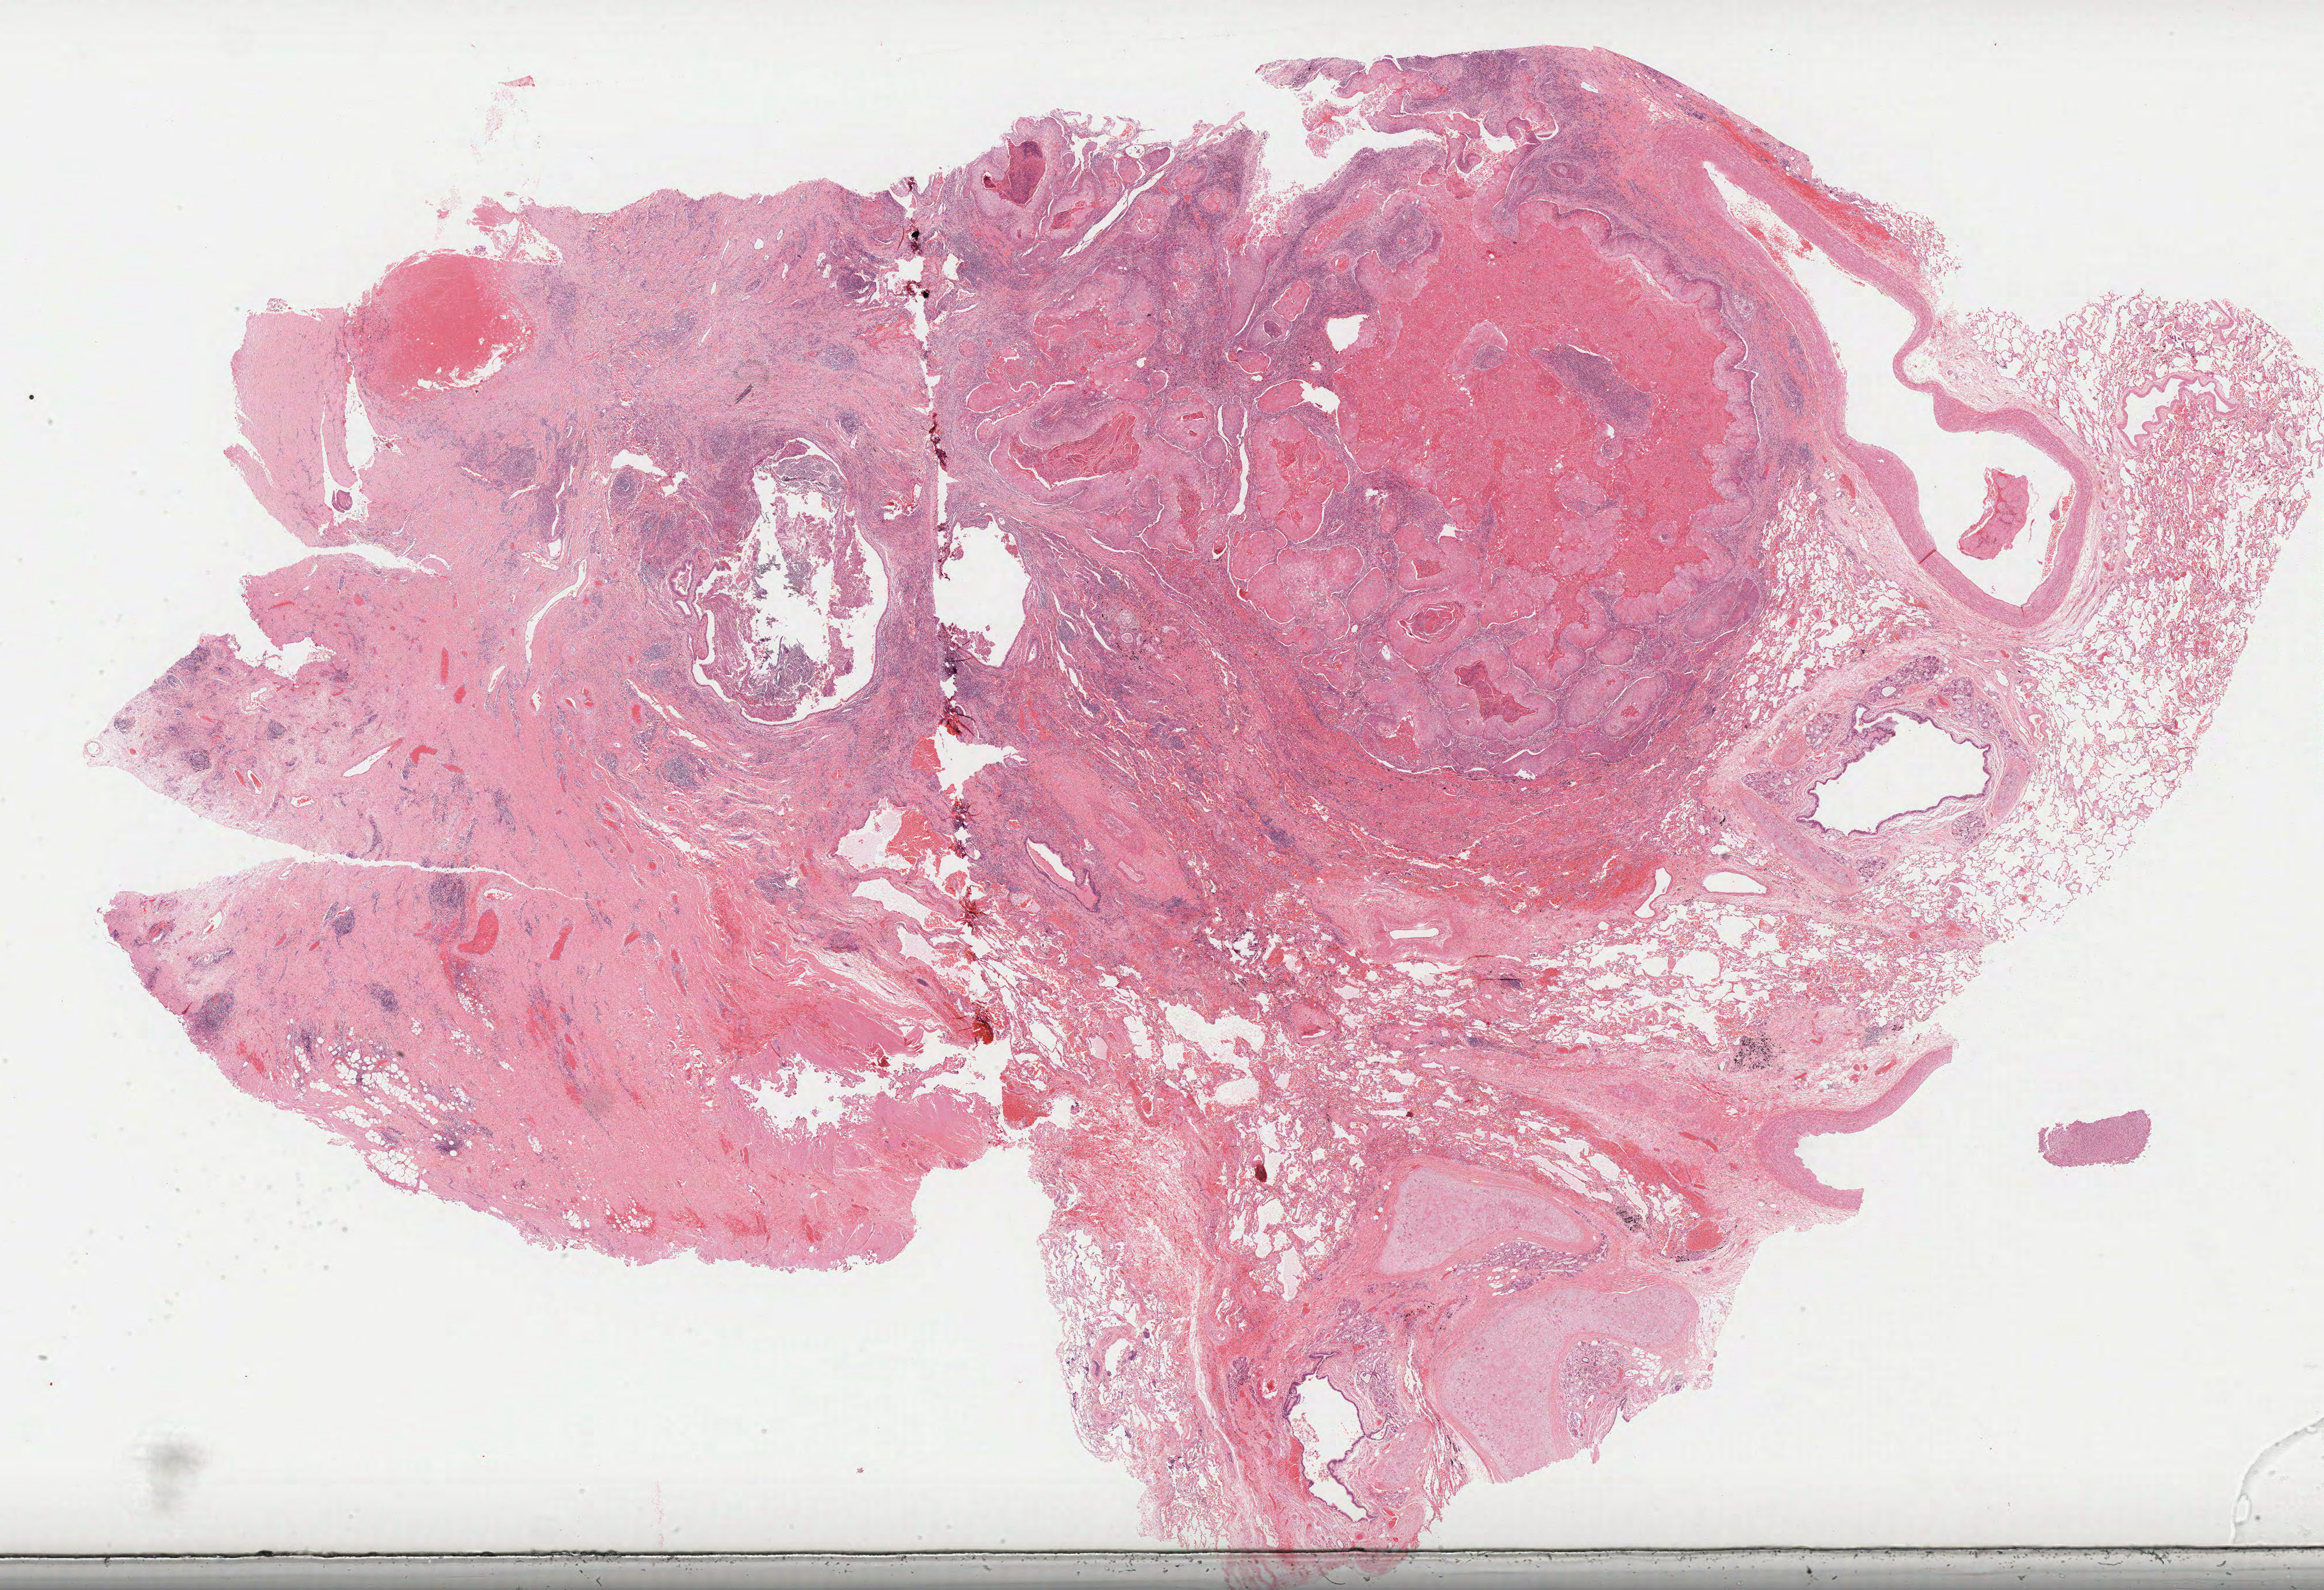
H&E whole-slide image, whole scanned area (about 32.3 x 22.1 mm) shown as a low-resolution overview, formalin-fixed paraffin-embedded (FFPE) diagnostic section, primary tumour sample from the lung. Male patient; age at initial diagnosis 67 years.
Laterality: left. AJCC pathologic stage: IA. Diagnosis: Squamous cell carcinoma, NOS (upper lobe, lung).